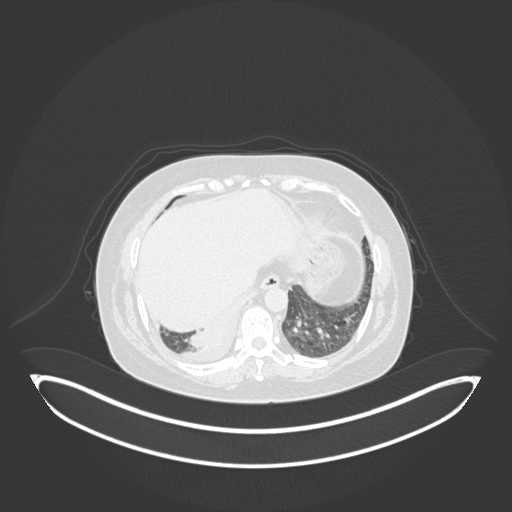
Chest CT, one axial slice; slice 27 of 231 in the series (ordered by position); reconstruction kernel B30f; lung window (W 1500 / L -600 HU); 1 mm slice thickness; 512 × 512 image matrix, field of view 500 × 500 mm. Female patient, age 56 years. Case-level facts recorded for this patient, not image findings: clinical TNM (as recorded): T2b N1 M0.
Structures marked on this image (bounding box drawn by a radiologist):
- lung tumour (recorded histology: small cell carcinoma): bounding box <182,318,226,354> (left, top, right, bottom; pixels)